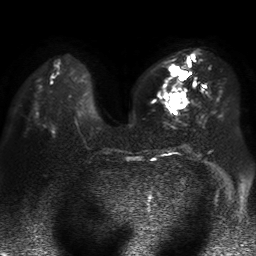
Breast MRI, one axial slice. Slice 20 of 50 in the series (ordered by position). Diffusion-weighted series; image 2 of 4 stored at this slice position (different b-values; order by instance number). 1.5 T. 256 × 256 image matrix. Female patient.
Outlined on this slice (outlined manually by an expert reader):
- tumour on diffusion-weighted imaging: box from (x=170, y=65) to (x=186, y=108) px